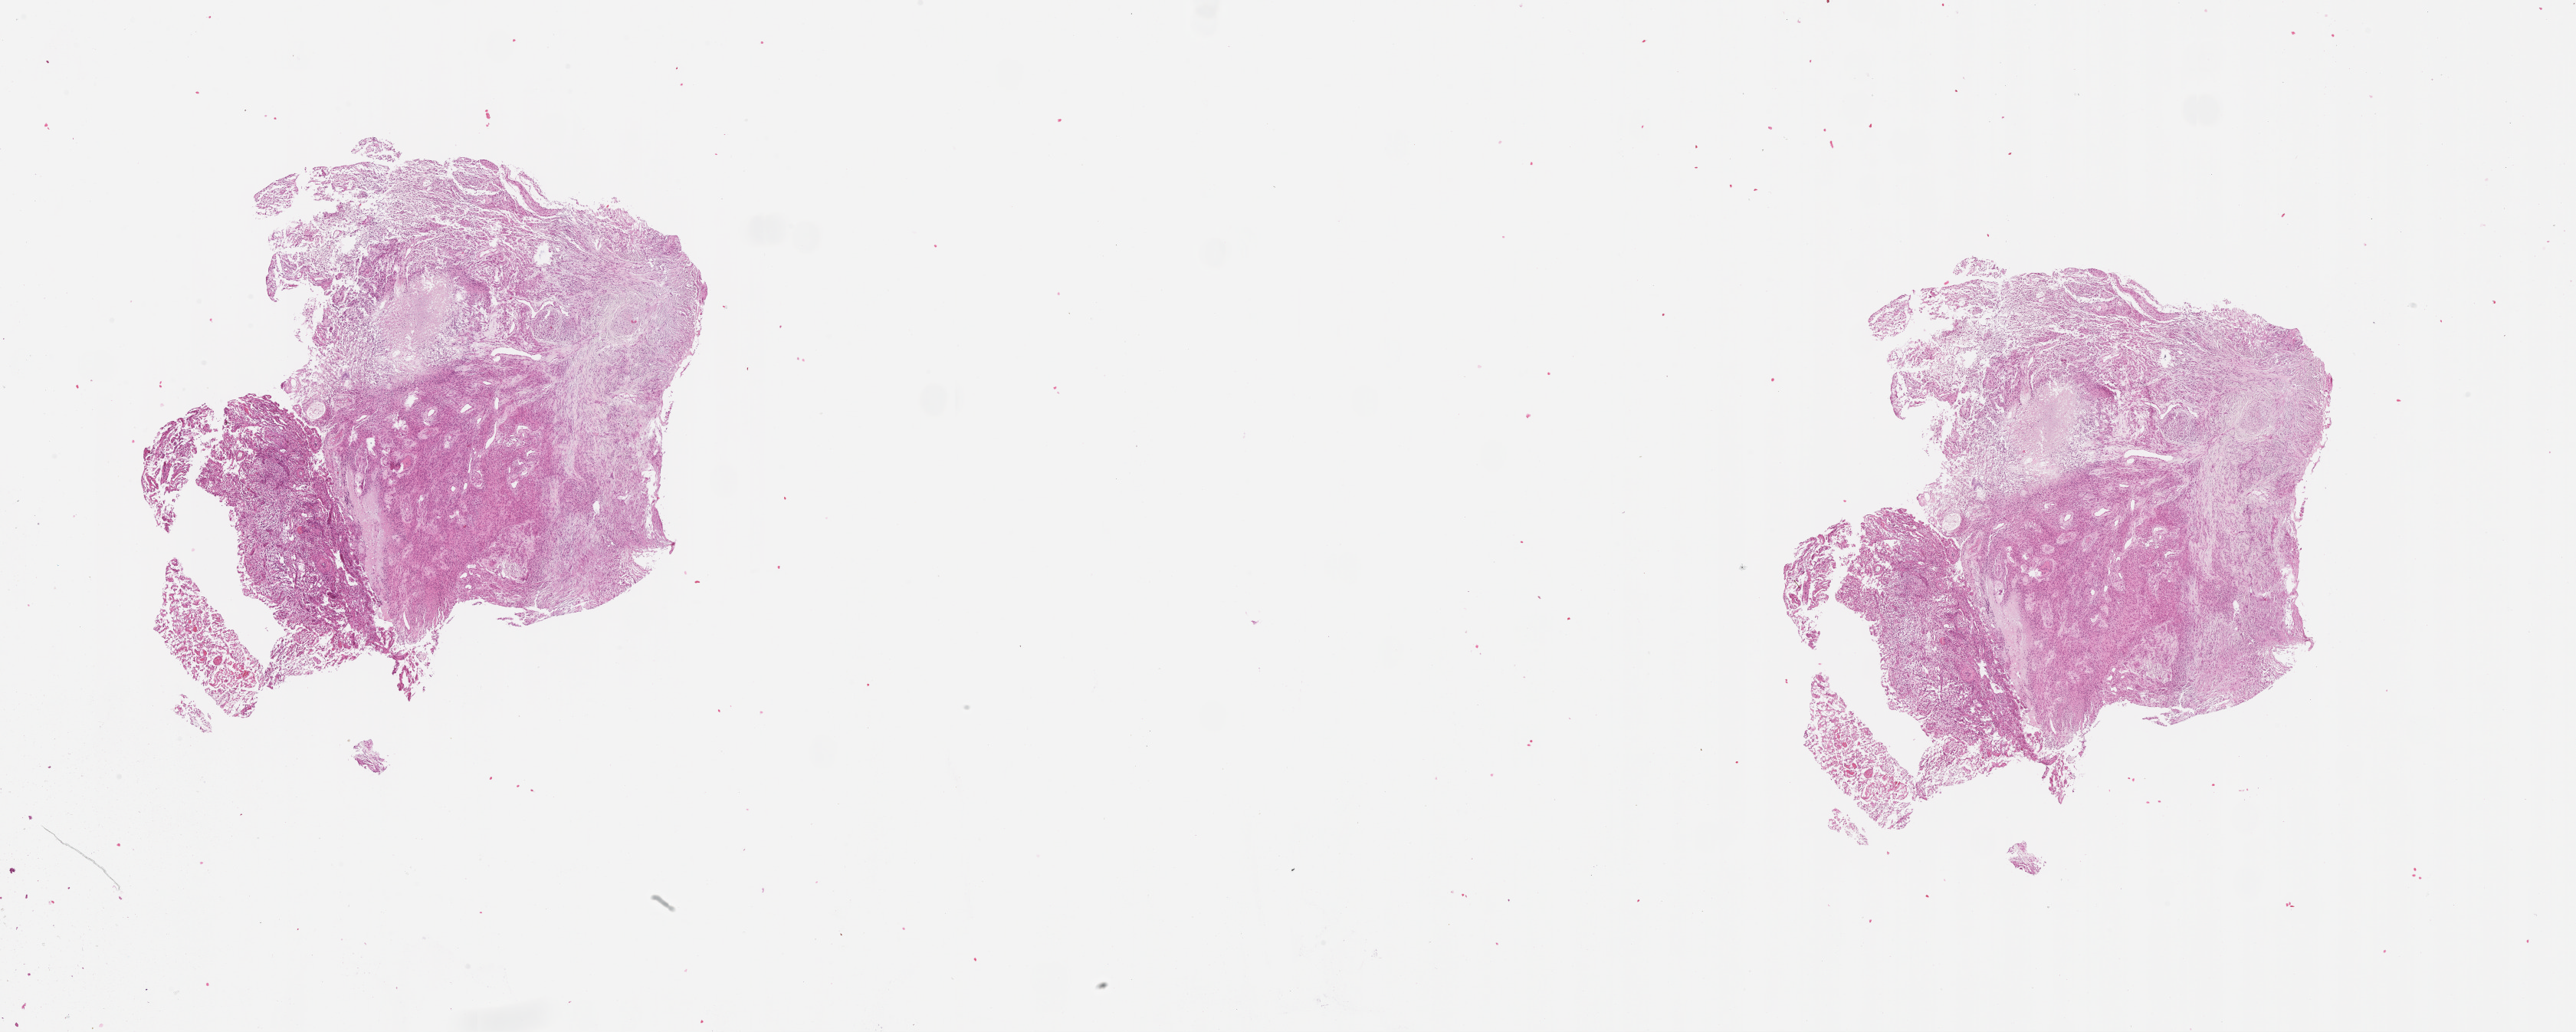
Hematoxylin and eosin (H&E) stained whole-slide image — a low-resolution overview of the entire scanned area, about 27.1 x 10.8 mm (slide scanned at 20x), tumour tissue sample, brain. 72-year-old male patient.
Histologic diagnosis: Glioblastoma.